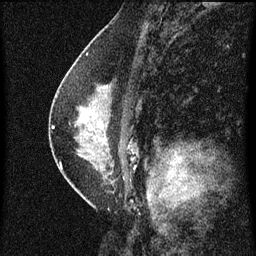
Breast MRI (dynamic contrast-enhanced), one sagittal slice. Slice 36 of 60 in the series (ordered by position). Dynamic contrast-enhanced series, image 2 of 3 at this slice position (ordered by acquisition). 1.5 T. TE 4.2 ms, TR 8 ms. 256 × 256 image matrix. Female patient, age 47 years.
Outlined on this slice (semi-automatic segmentation, software-assisted and operator-edited):
- analysis volume of interest (the breast-tissue region the enhancement analysis was run in; not a lesion): bounding box [x1, y1, x2, y2] px = [54, 80, 135, 187]
- tumour enhancement mask (voxels above the 70 % enhancement threshold inside the analysis volume of interest): [54, 126, 63, 169]